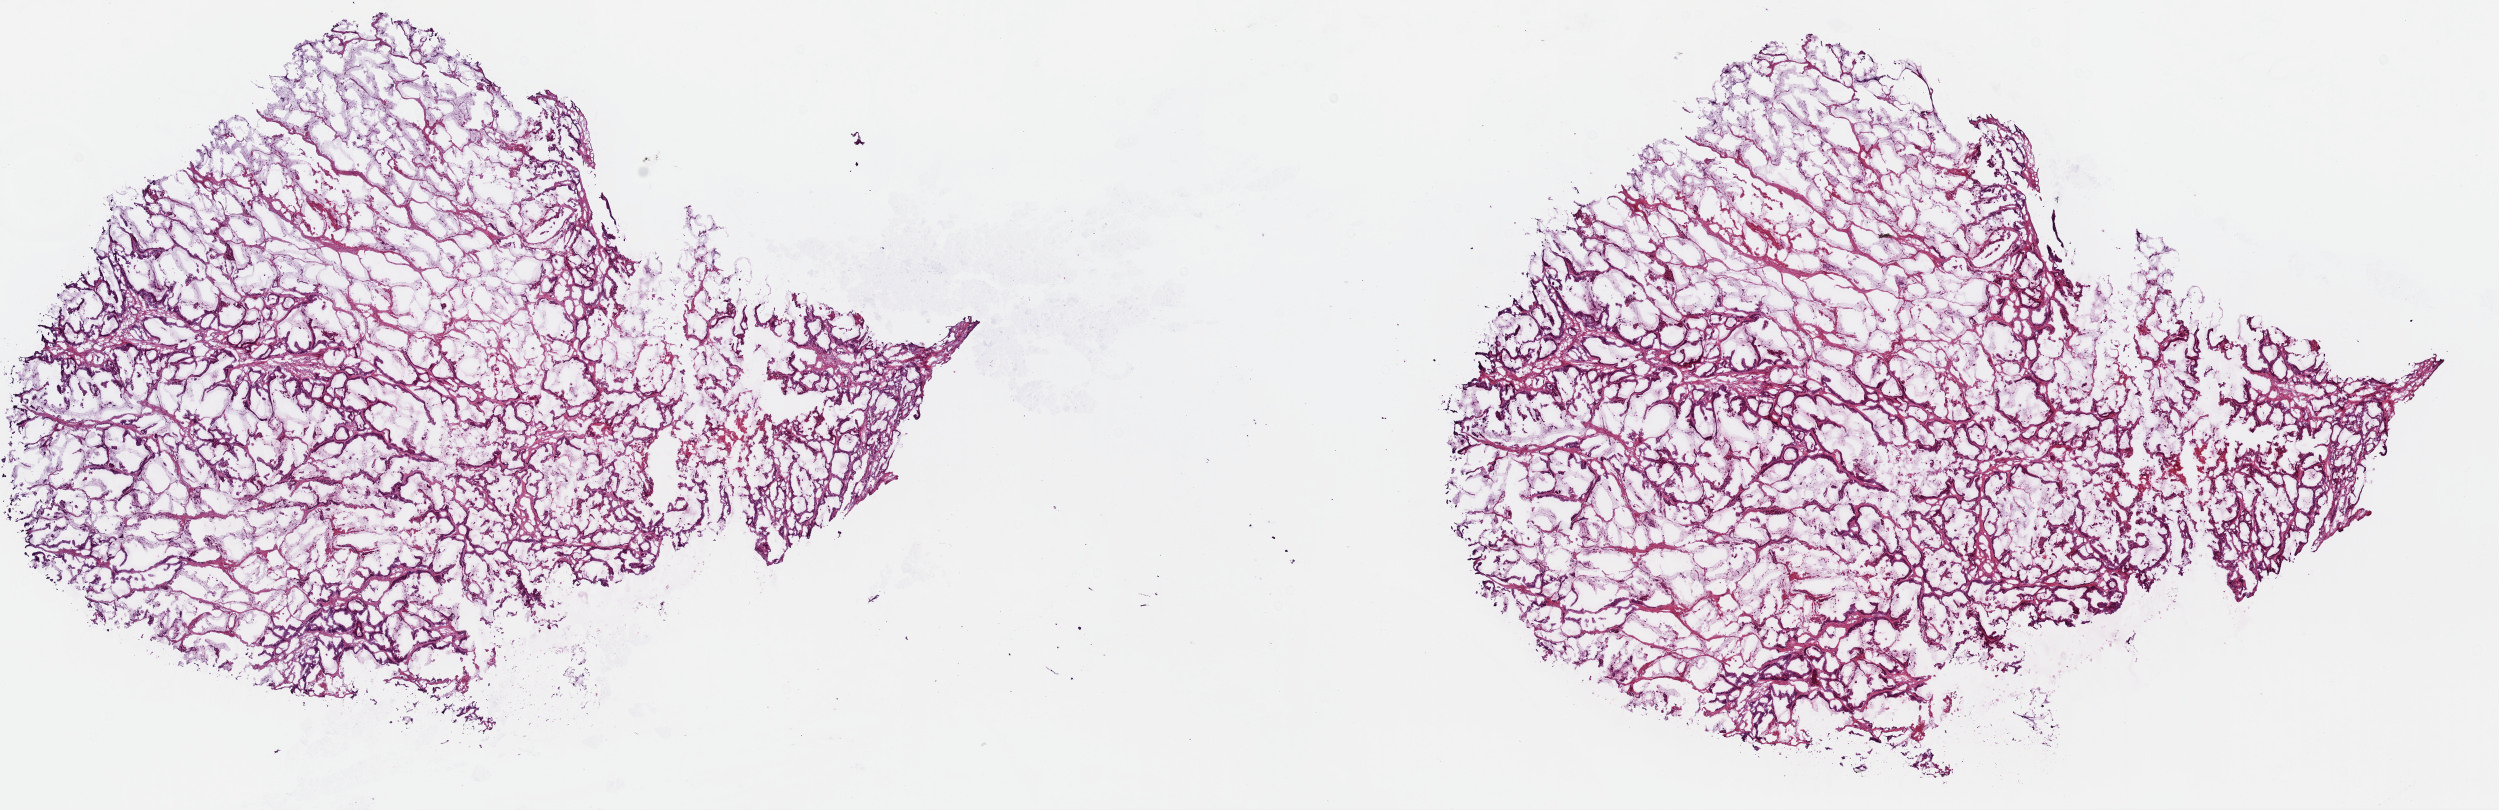
H&E-stained whole-slide image — shown as a low-resolution overview of the whole scanned area (about 19.7 x 6.4 mm); frozen section from the top of the tissue portion; sample: primary tumour, colon. Patient: male, age at initial diagnosis 68 years. Slide review estimates, as recorded: tumour cells 70%, tumour nuclei 80%, normal cells 0%, stromal cells 20%, necrosis 10%. Infiltration values recorded for this section: lymphocyte infiltration 1%, monocyte infiltration 0%, neutrophil infiltration 0%.
- lymph nodes positive (case pathology): 4 of 22 examined
- AJCC pathologic stage: IIIC (6th edition)
- diagnosis: Mucinous adenocarcinoma